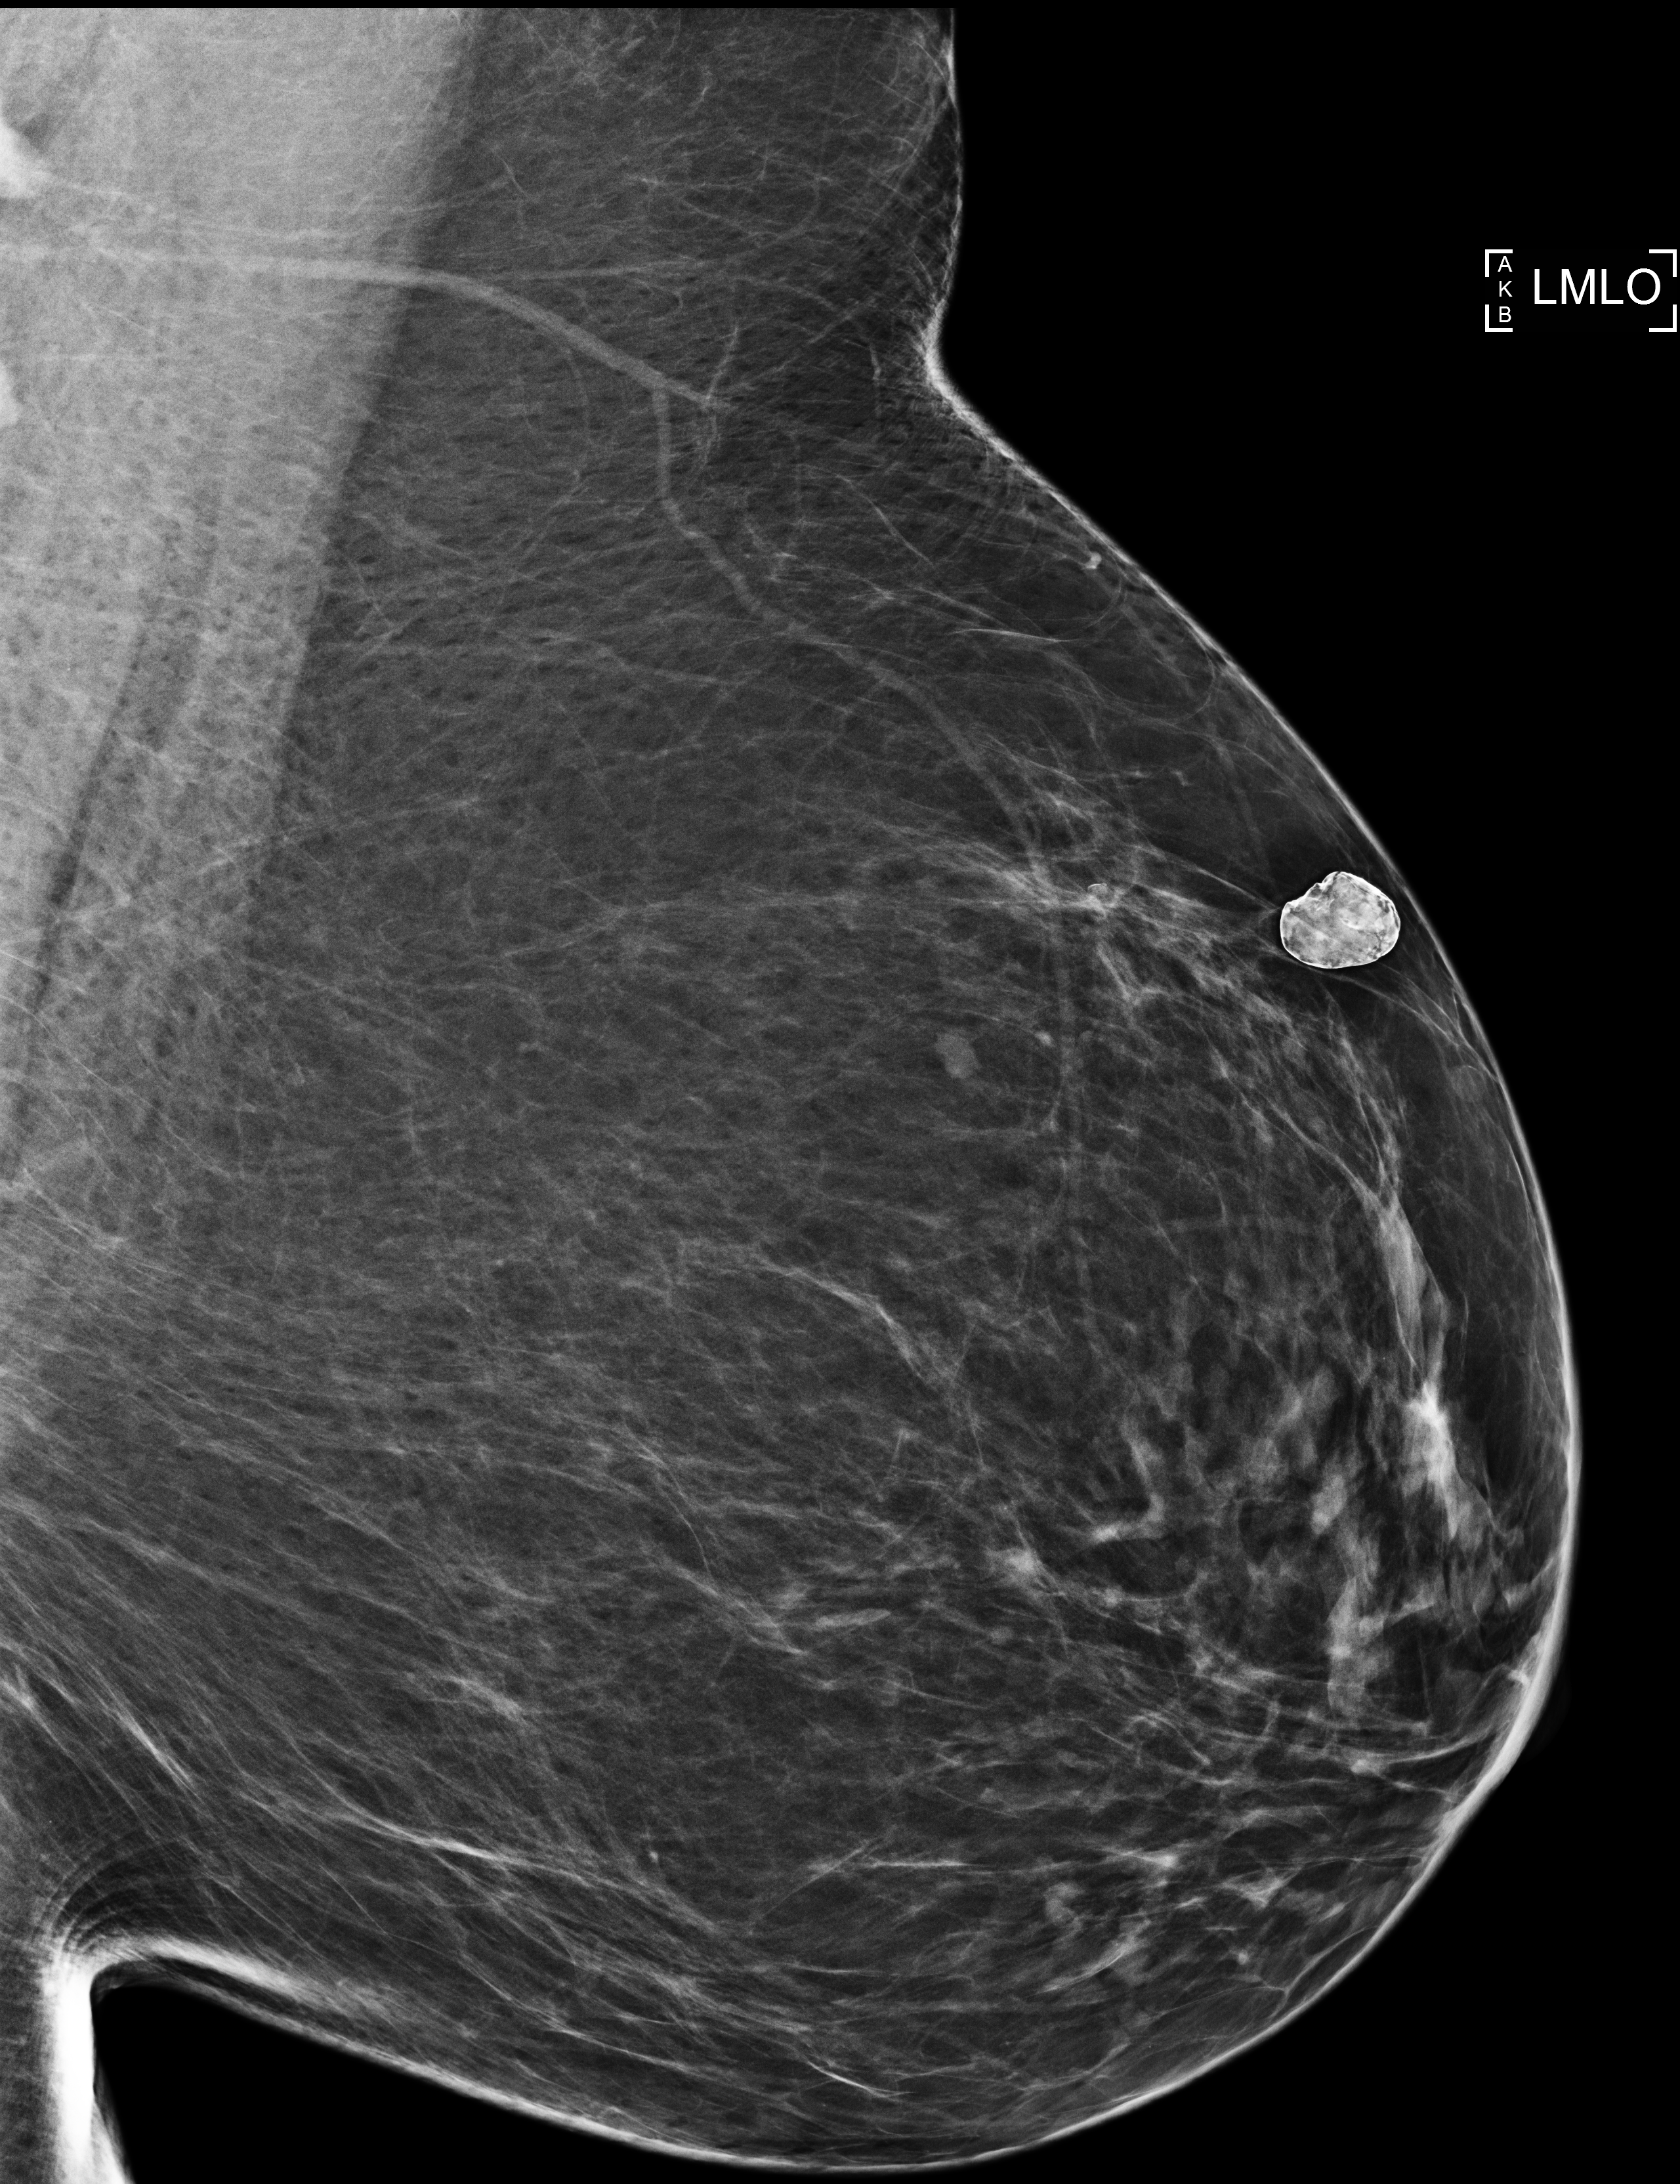
Digital mammogram (FFDM); left breast; medio-lateral oblique projection; annual screening mammography examination; compressed breast thickness 73 mm. Patient: female, 66 years.
- BI-RADS breast density category at the screening exam (both breasts, scale 1–4): 2
- final BI-RADS category for the screening round (tomosynthesis exam, both breasts): category 1
- recall: no recall after this screen